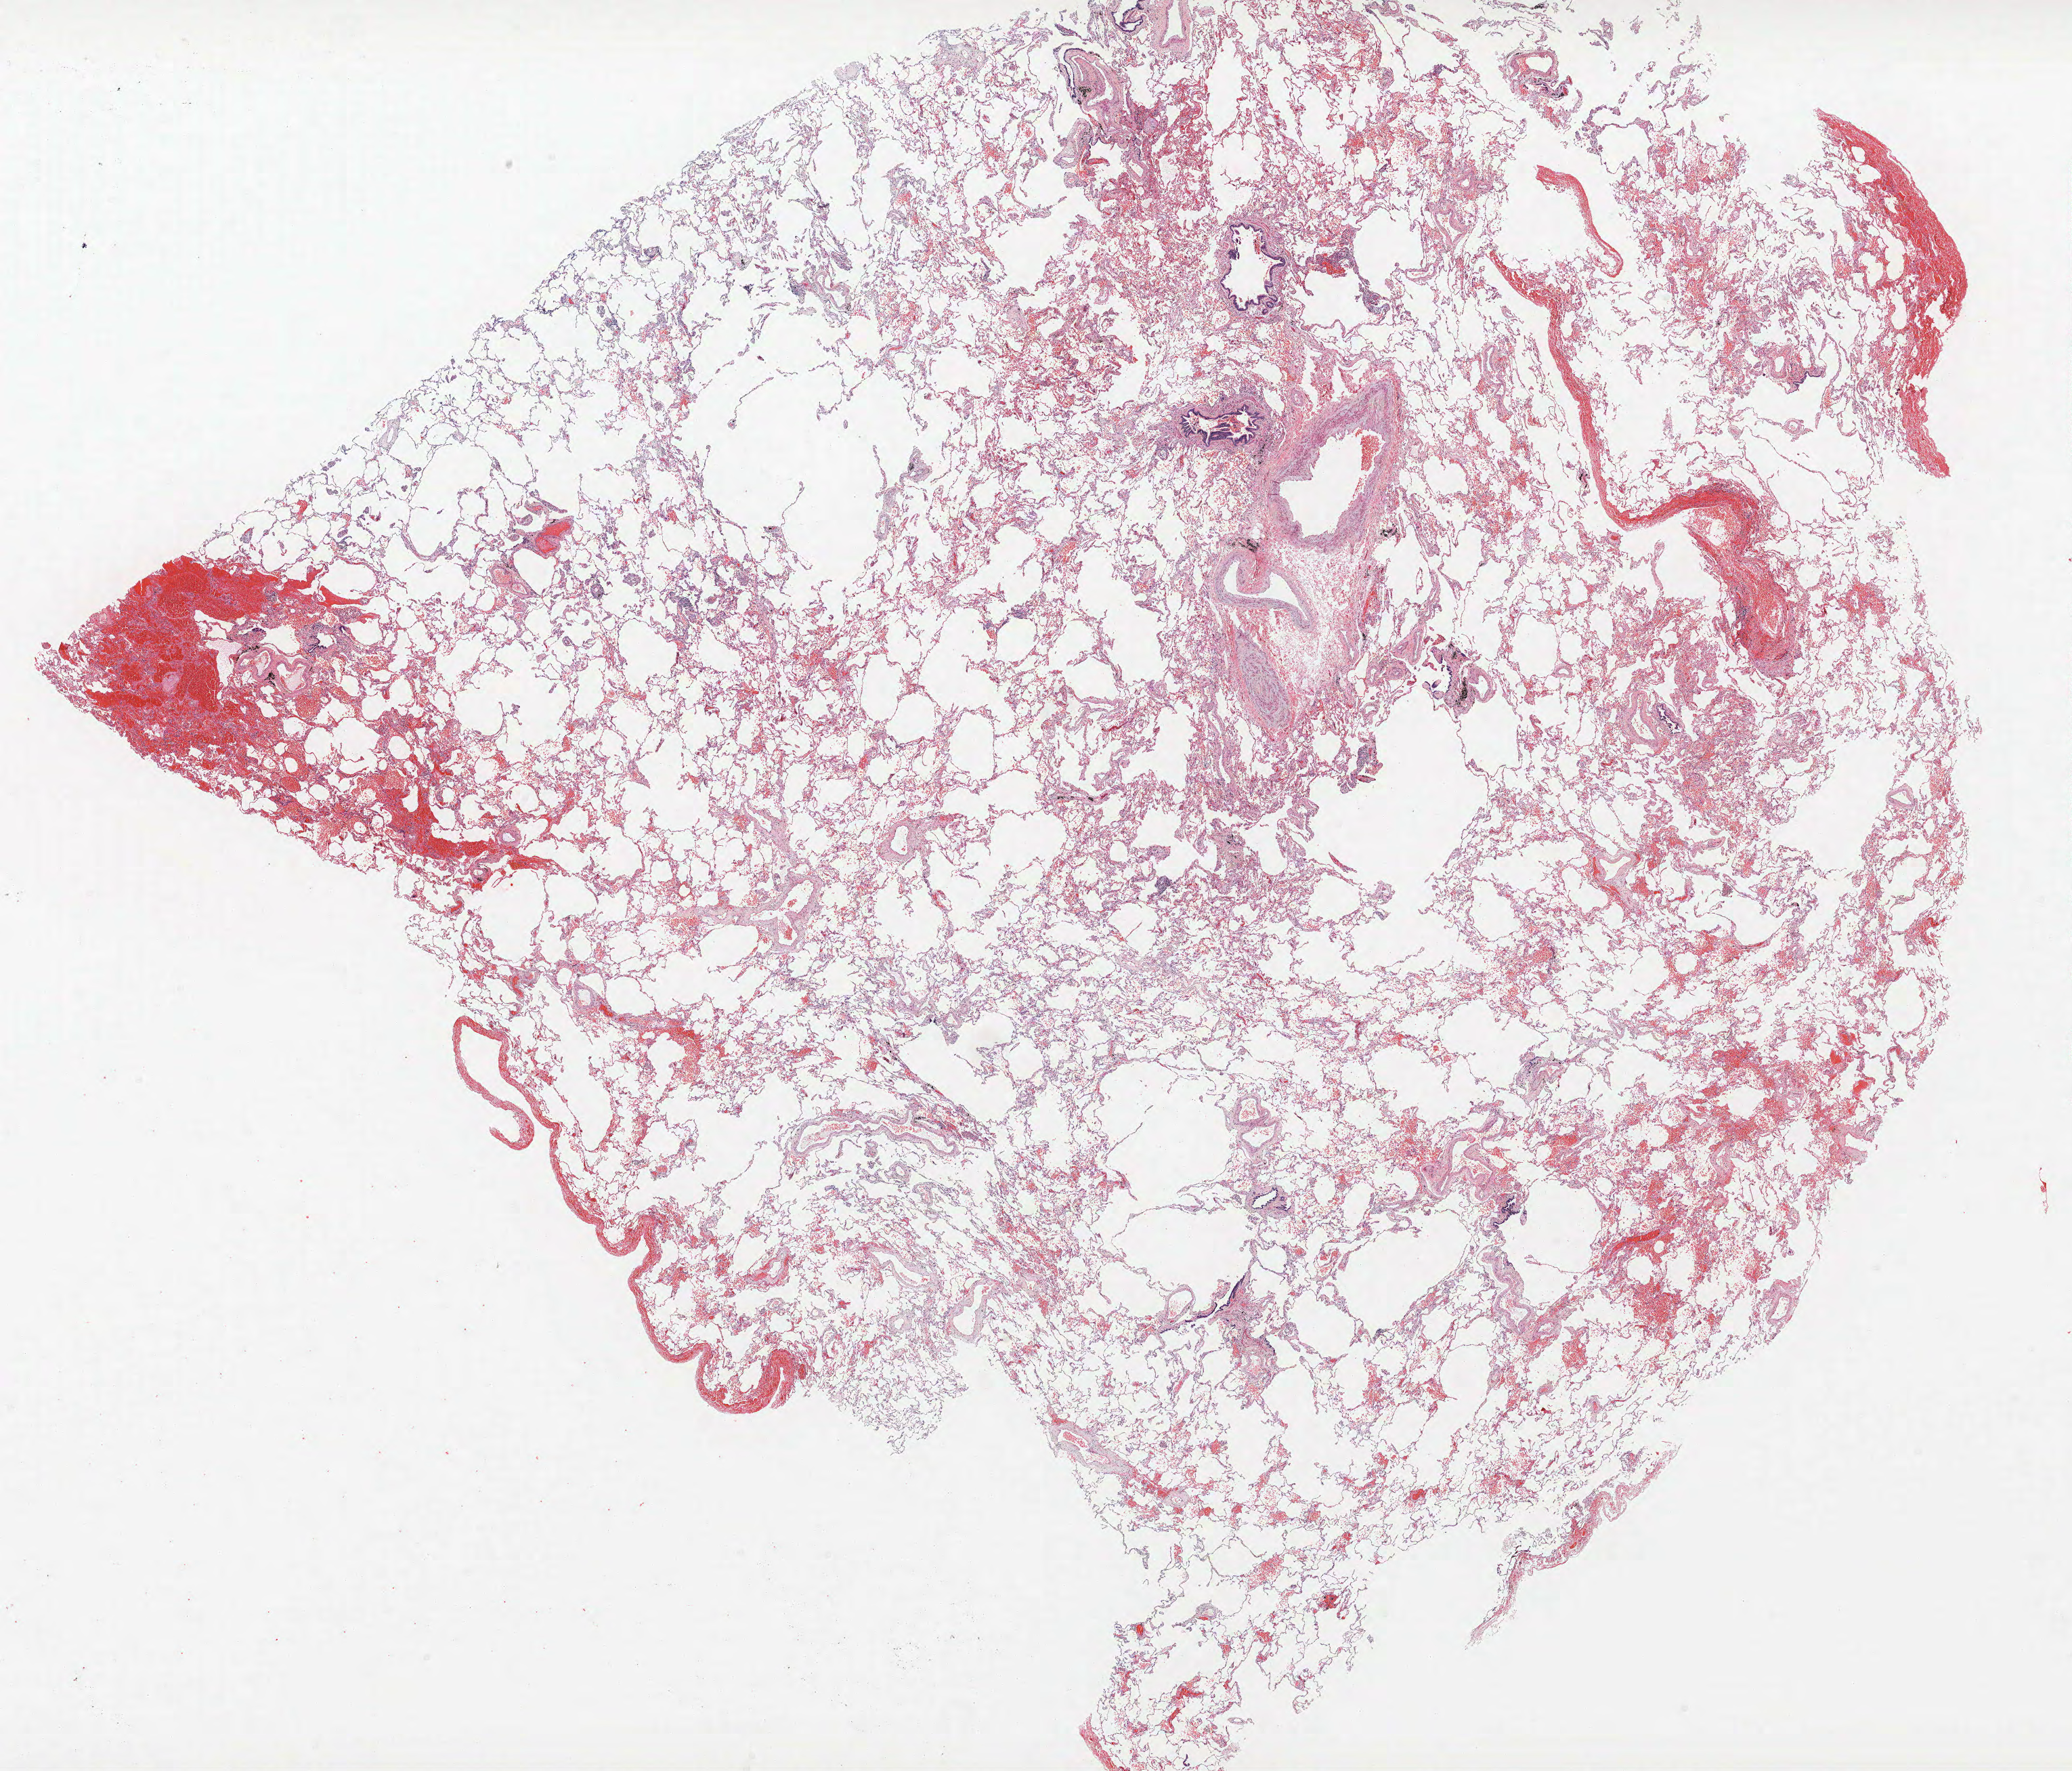
Whole-slide histology image, H&E-stained, low-resolution overview of the scanned area, about 24.5 x 20.9 mm. FFPE section. Lung. Male, age 69 at enrolment. Current smoker at enrolment. Grade: moderately differentiated (G2).
Stage (AJCC 6th edition): IIA. Tumour size (pathology): 20 mm. Primary tumour location (clinical record): right upper lobe. Participant's lung-cancer diagnosis: Adenocarcinoma, NOS.